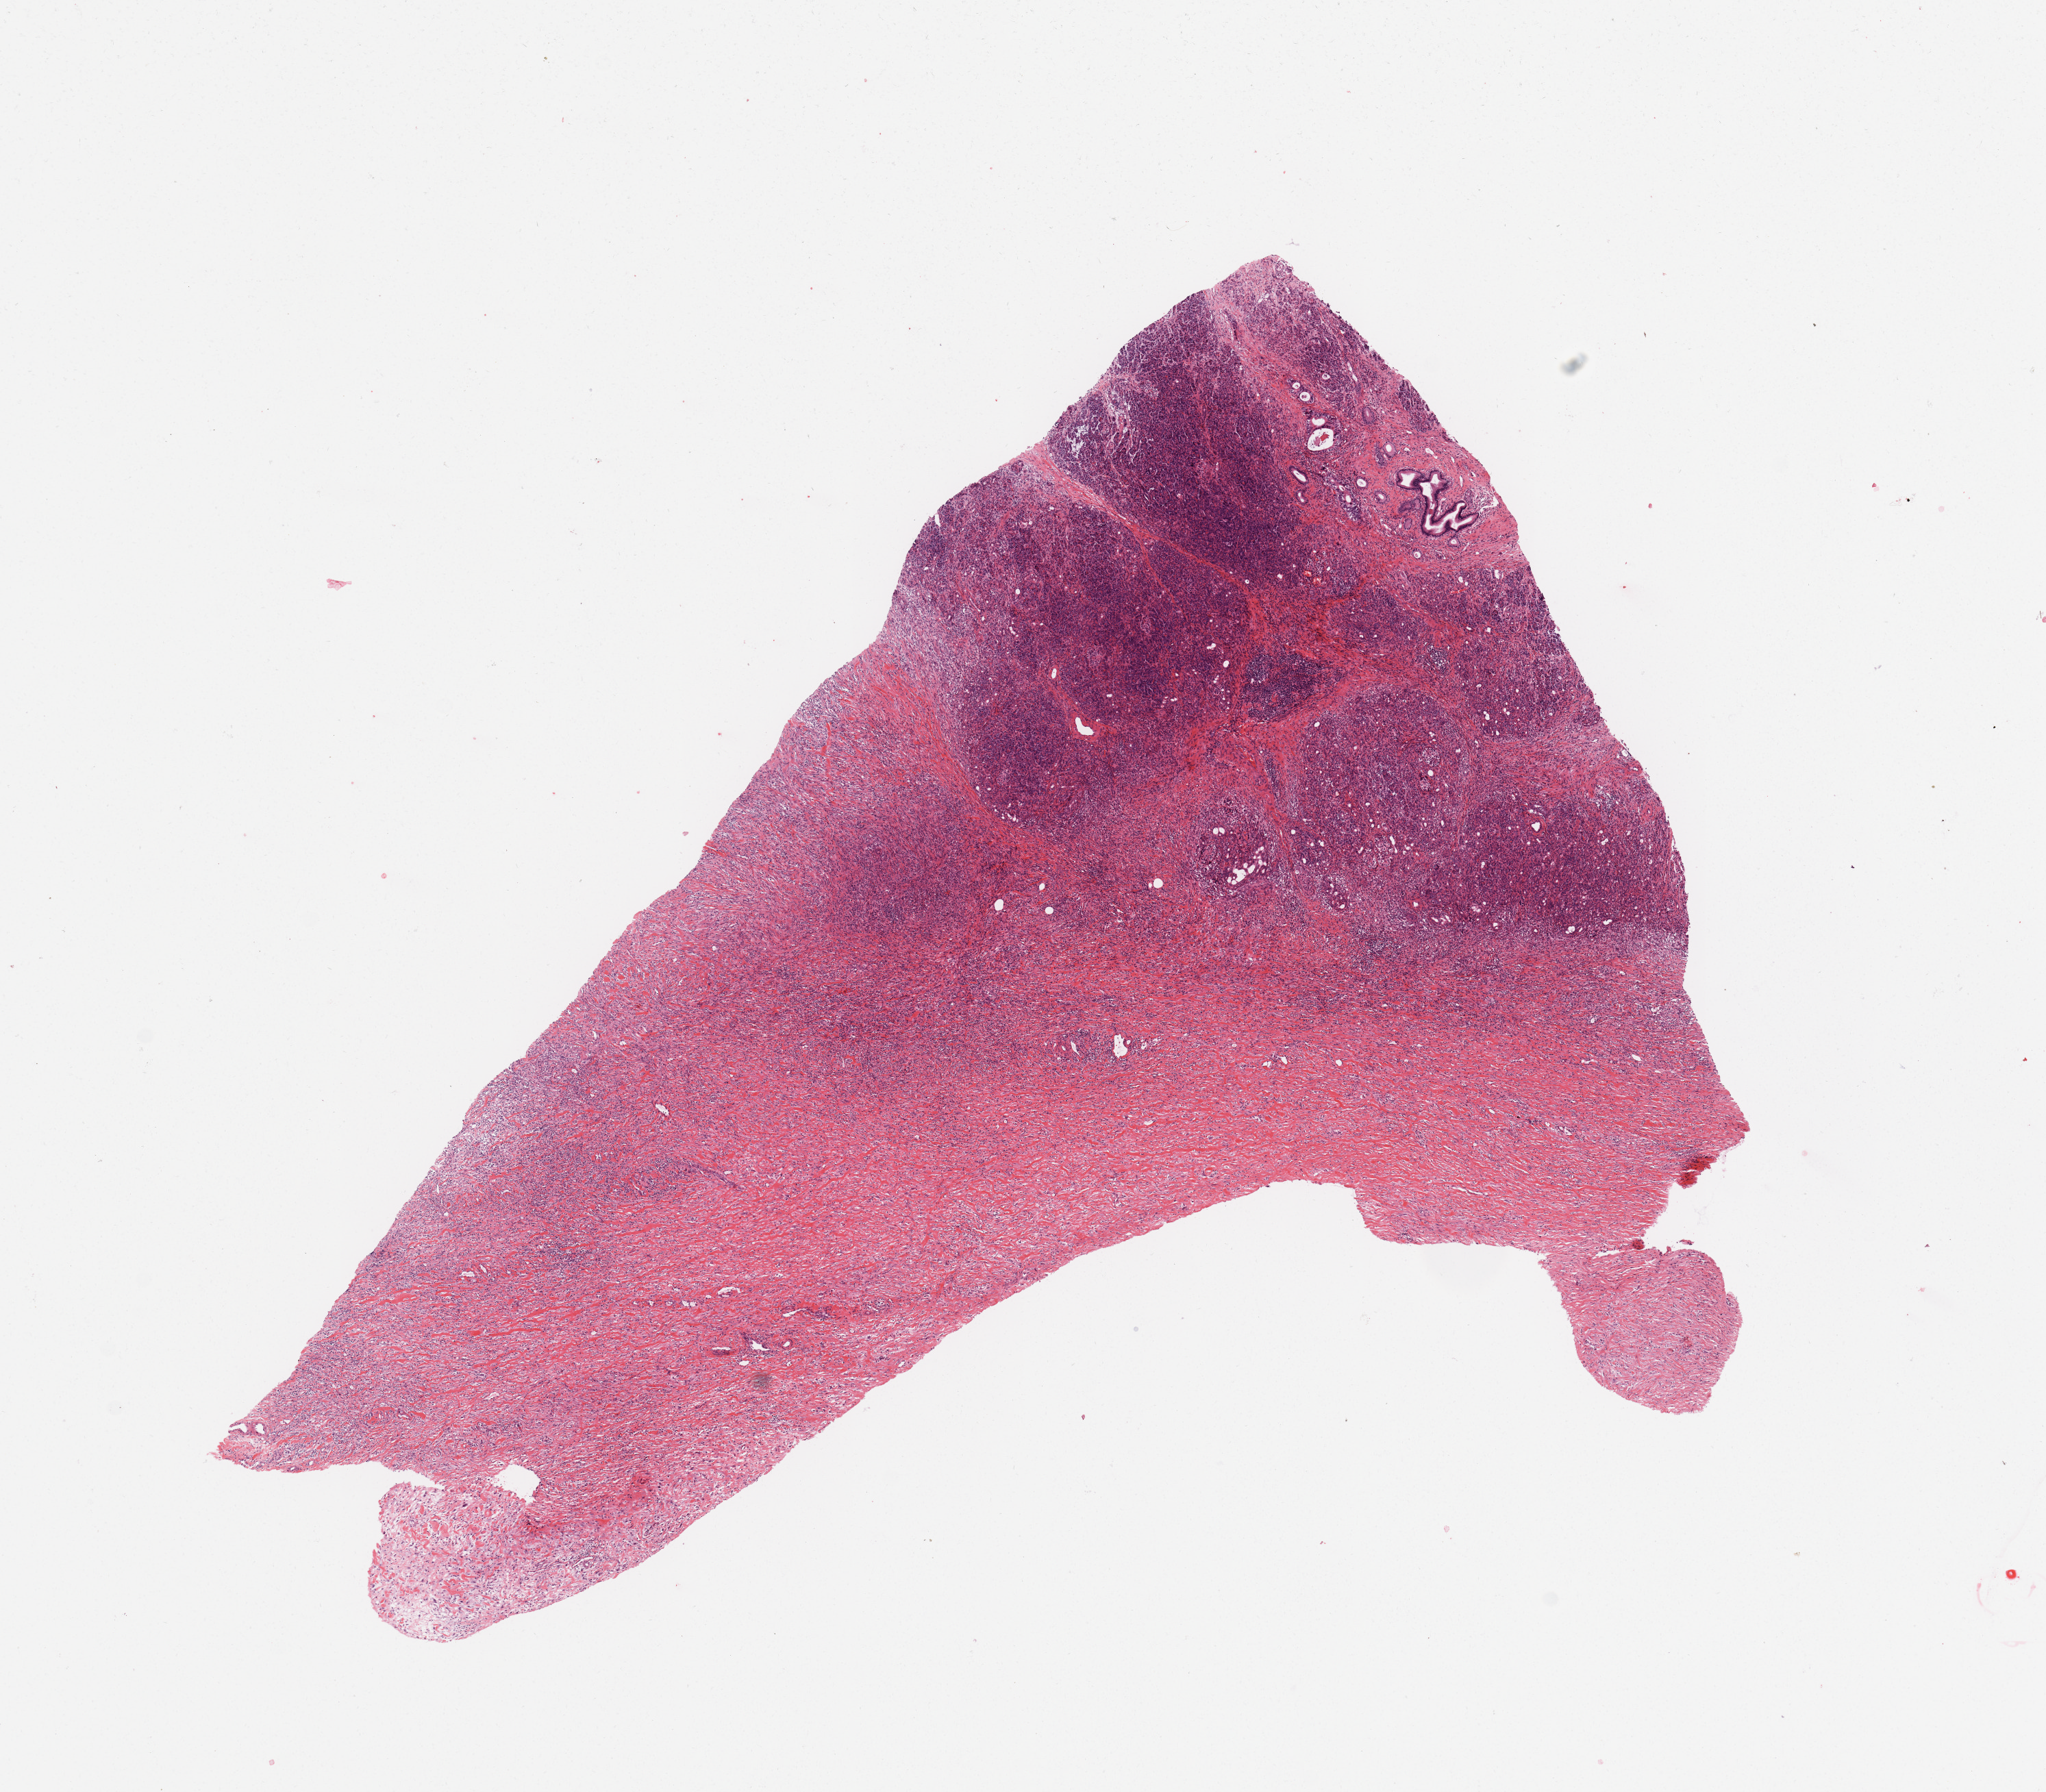
Digitized Hematoxylin and eosin (H&E) stained tissue section (whole slide), shown as a low-resolution overview of the whole scanned area (about 11.8 x 10.3 mm), tumour tissue sample, sampled site: pancreas. 63-year-old male patient.
Histologic diagnosis: Infiltrating duct carcinoma, NOS.